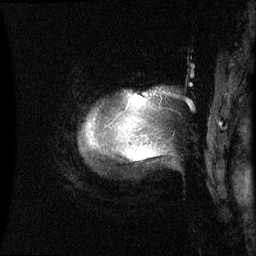
Breast MRI (dynamic contrast-enhanced), one sagittal slice. Slice 60 of 60 in the series (ordered by position). Dynamic contrast-enhanced series, image 2 of 3 at this slice position (ordered by acquisition). 1.5 T. TE 4.2 ms, TR 8.4 ms. 2.4 mm slice thickness. 256 × 256 image matrix, field of view 230 × 230 mm. Patient: female, 48 years.
Annotated regions visible in this slice (semi-automatic segmentation, software-assisted and operator-edited):
- analysis volume of interest (the breast-tissue region the enhancement analysis was run in; not a lesion): box from (x=87, y=94) to (x=153, y=160) px
- tumour enhancement mask (voxels above the 70 % enhancement threshold inside the analysis volume of interest): (x=129, y=98)–(x=133, y=103)